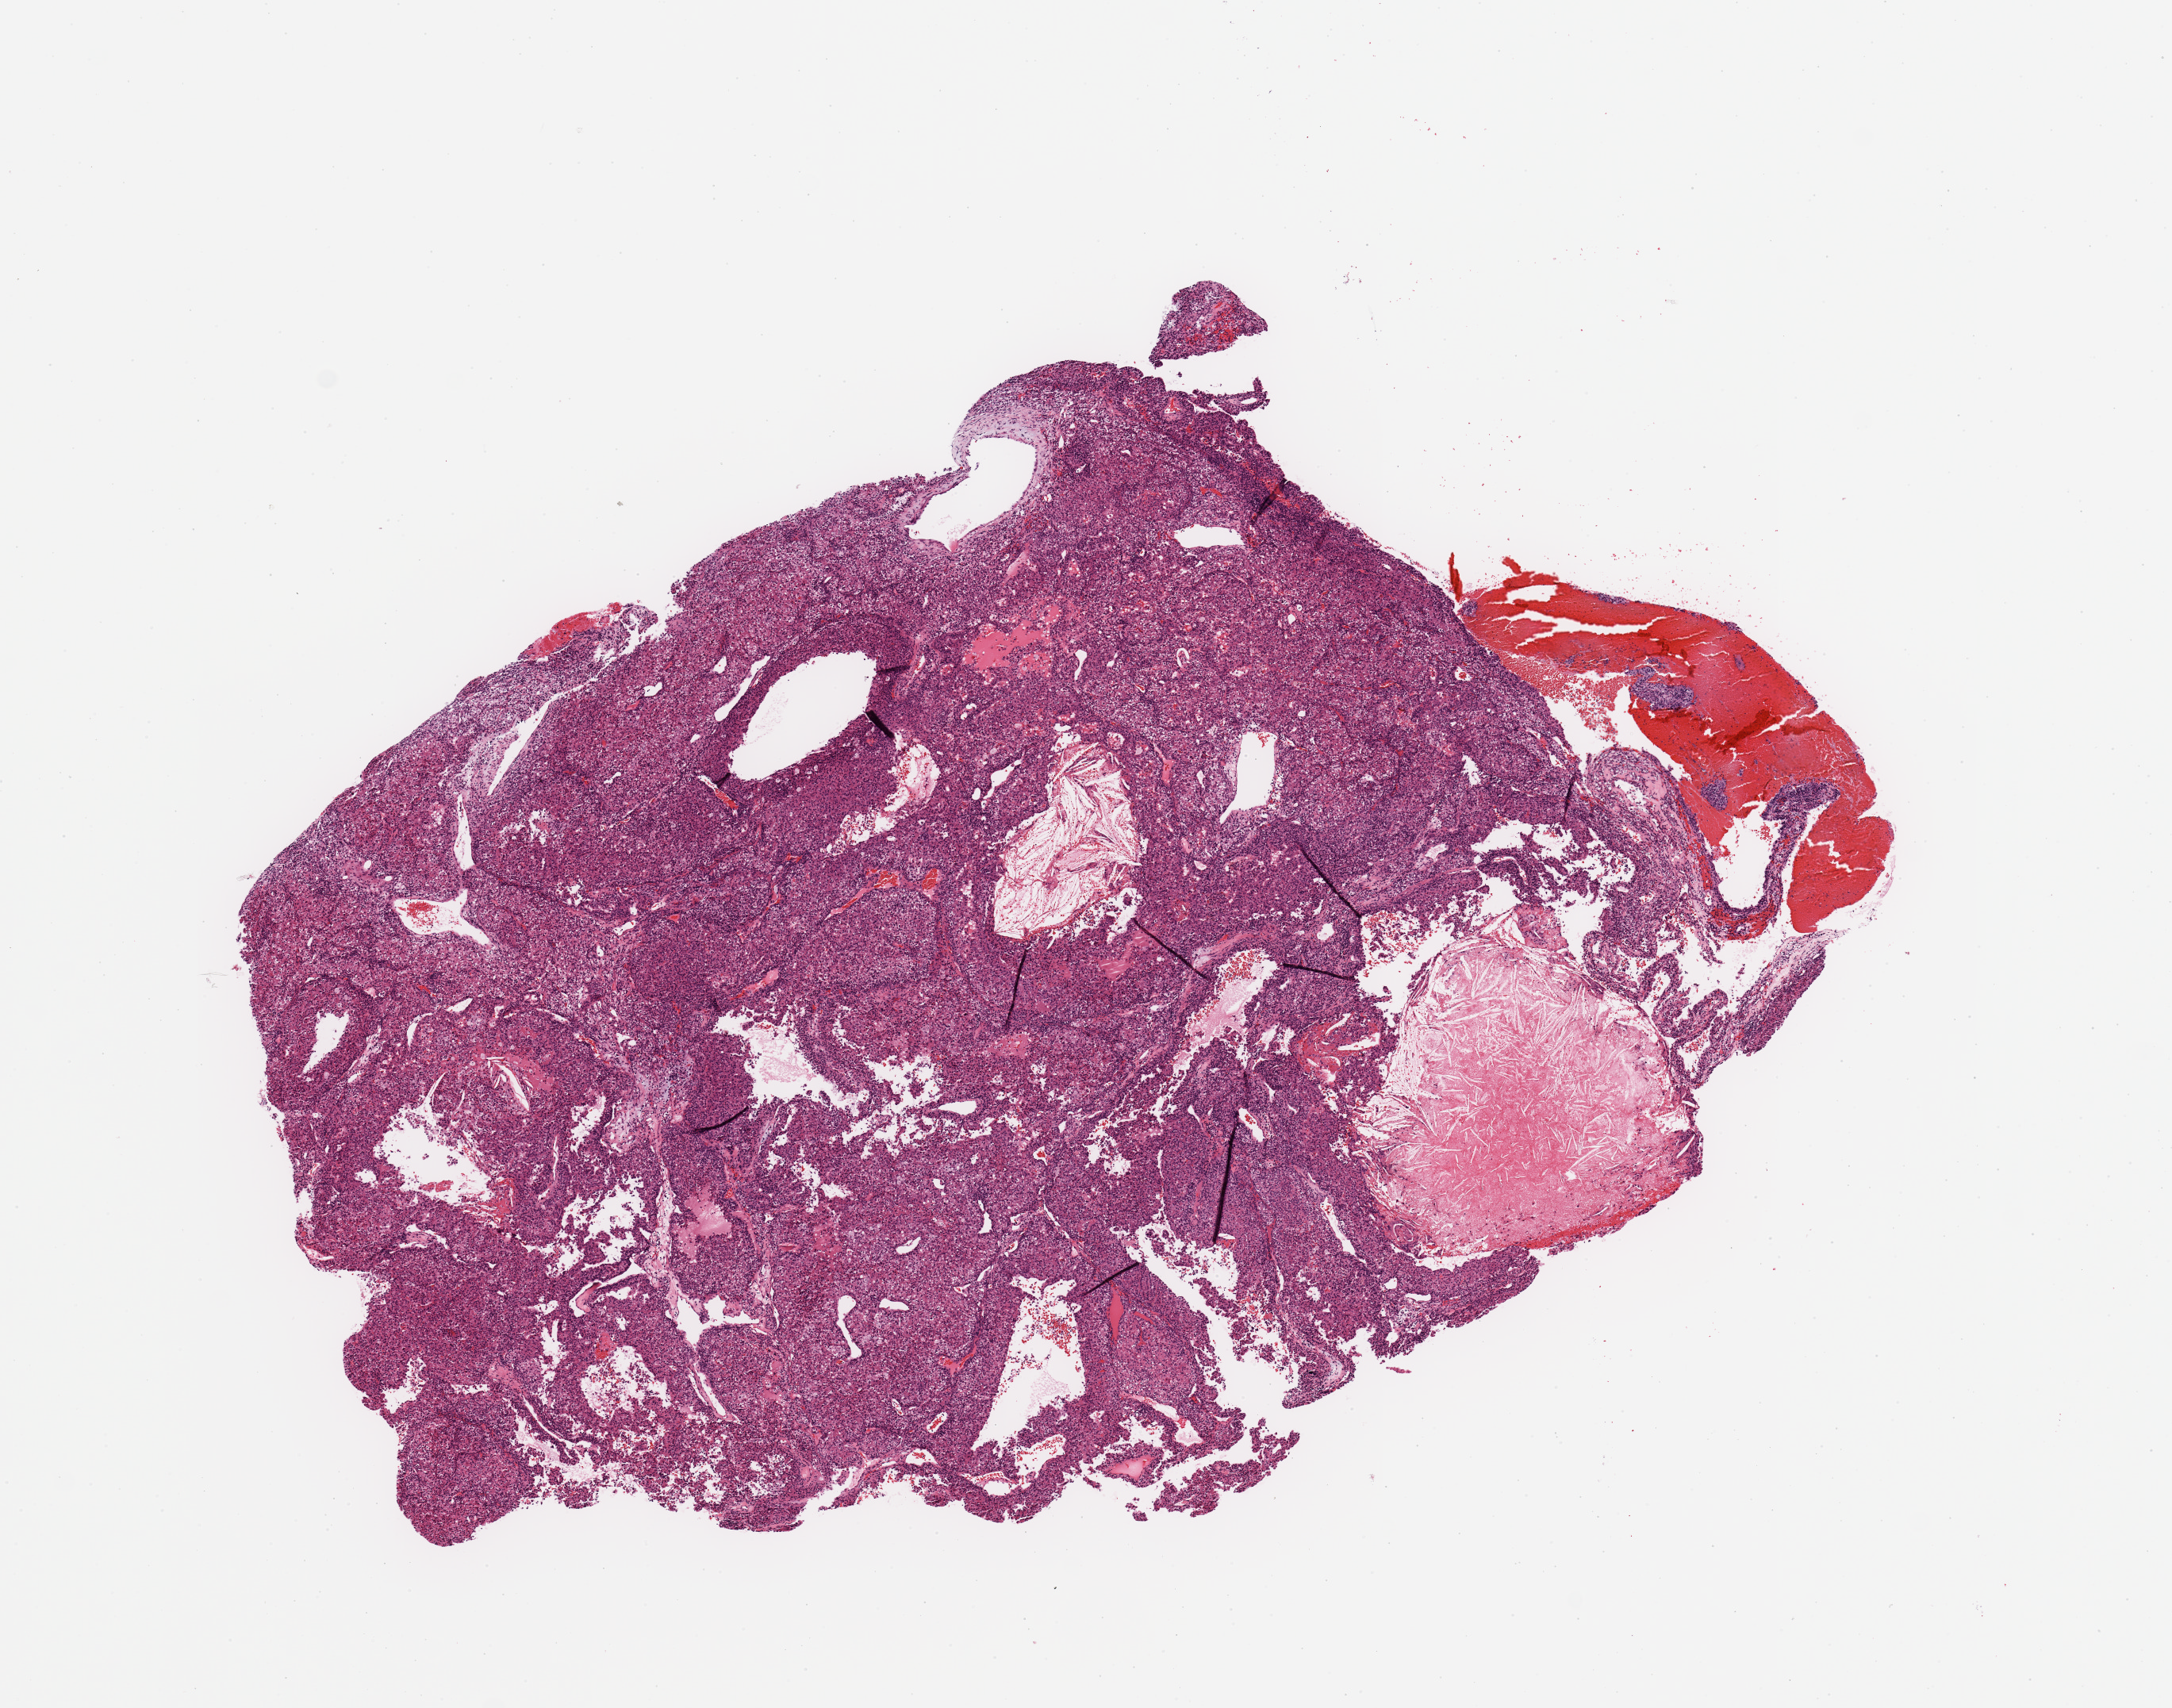
Digitized H&E tissue section (whole slide), shown as a low-resolution overview of the whole scanned area (about 10.8 x 8.5 mm). Tumour tissue sample, sampled site: kidney. Female, 60 y/o. Histologic grade: G3 (poorly differentiated). Composition of this section per pathologist review: tumour nuclei 90%, necrosis 5%.
Diagnosis: Renal cell carcinoma, NOS. AJCC pathologic stage: II.